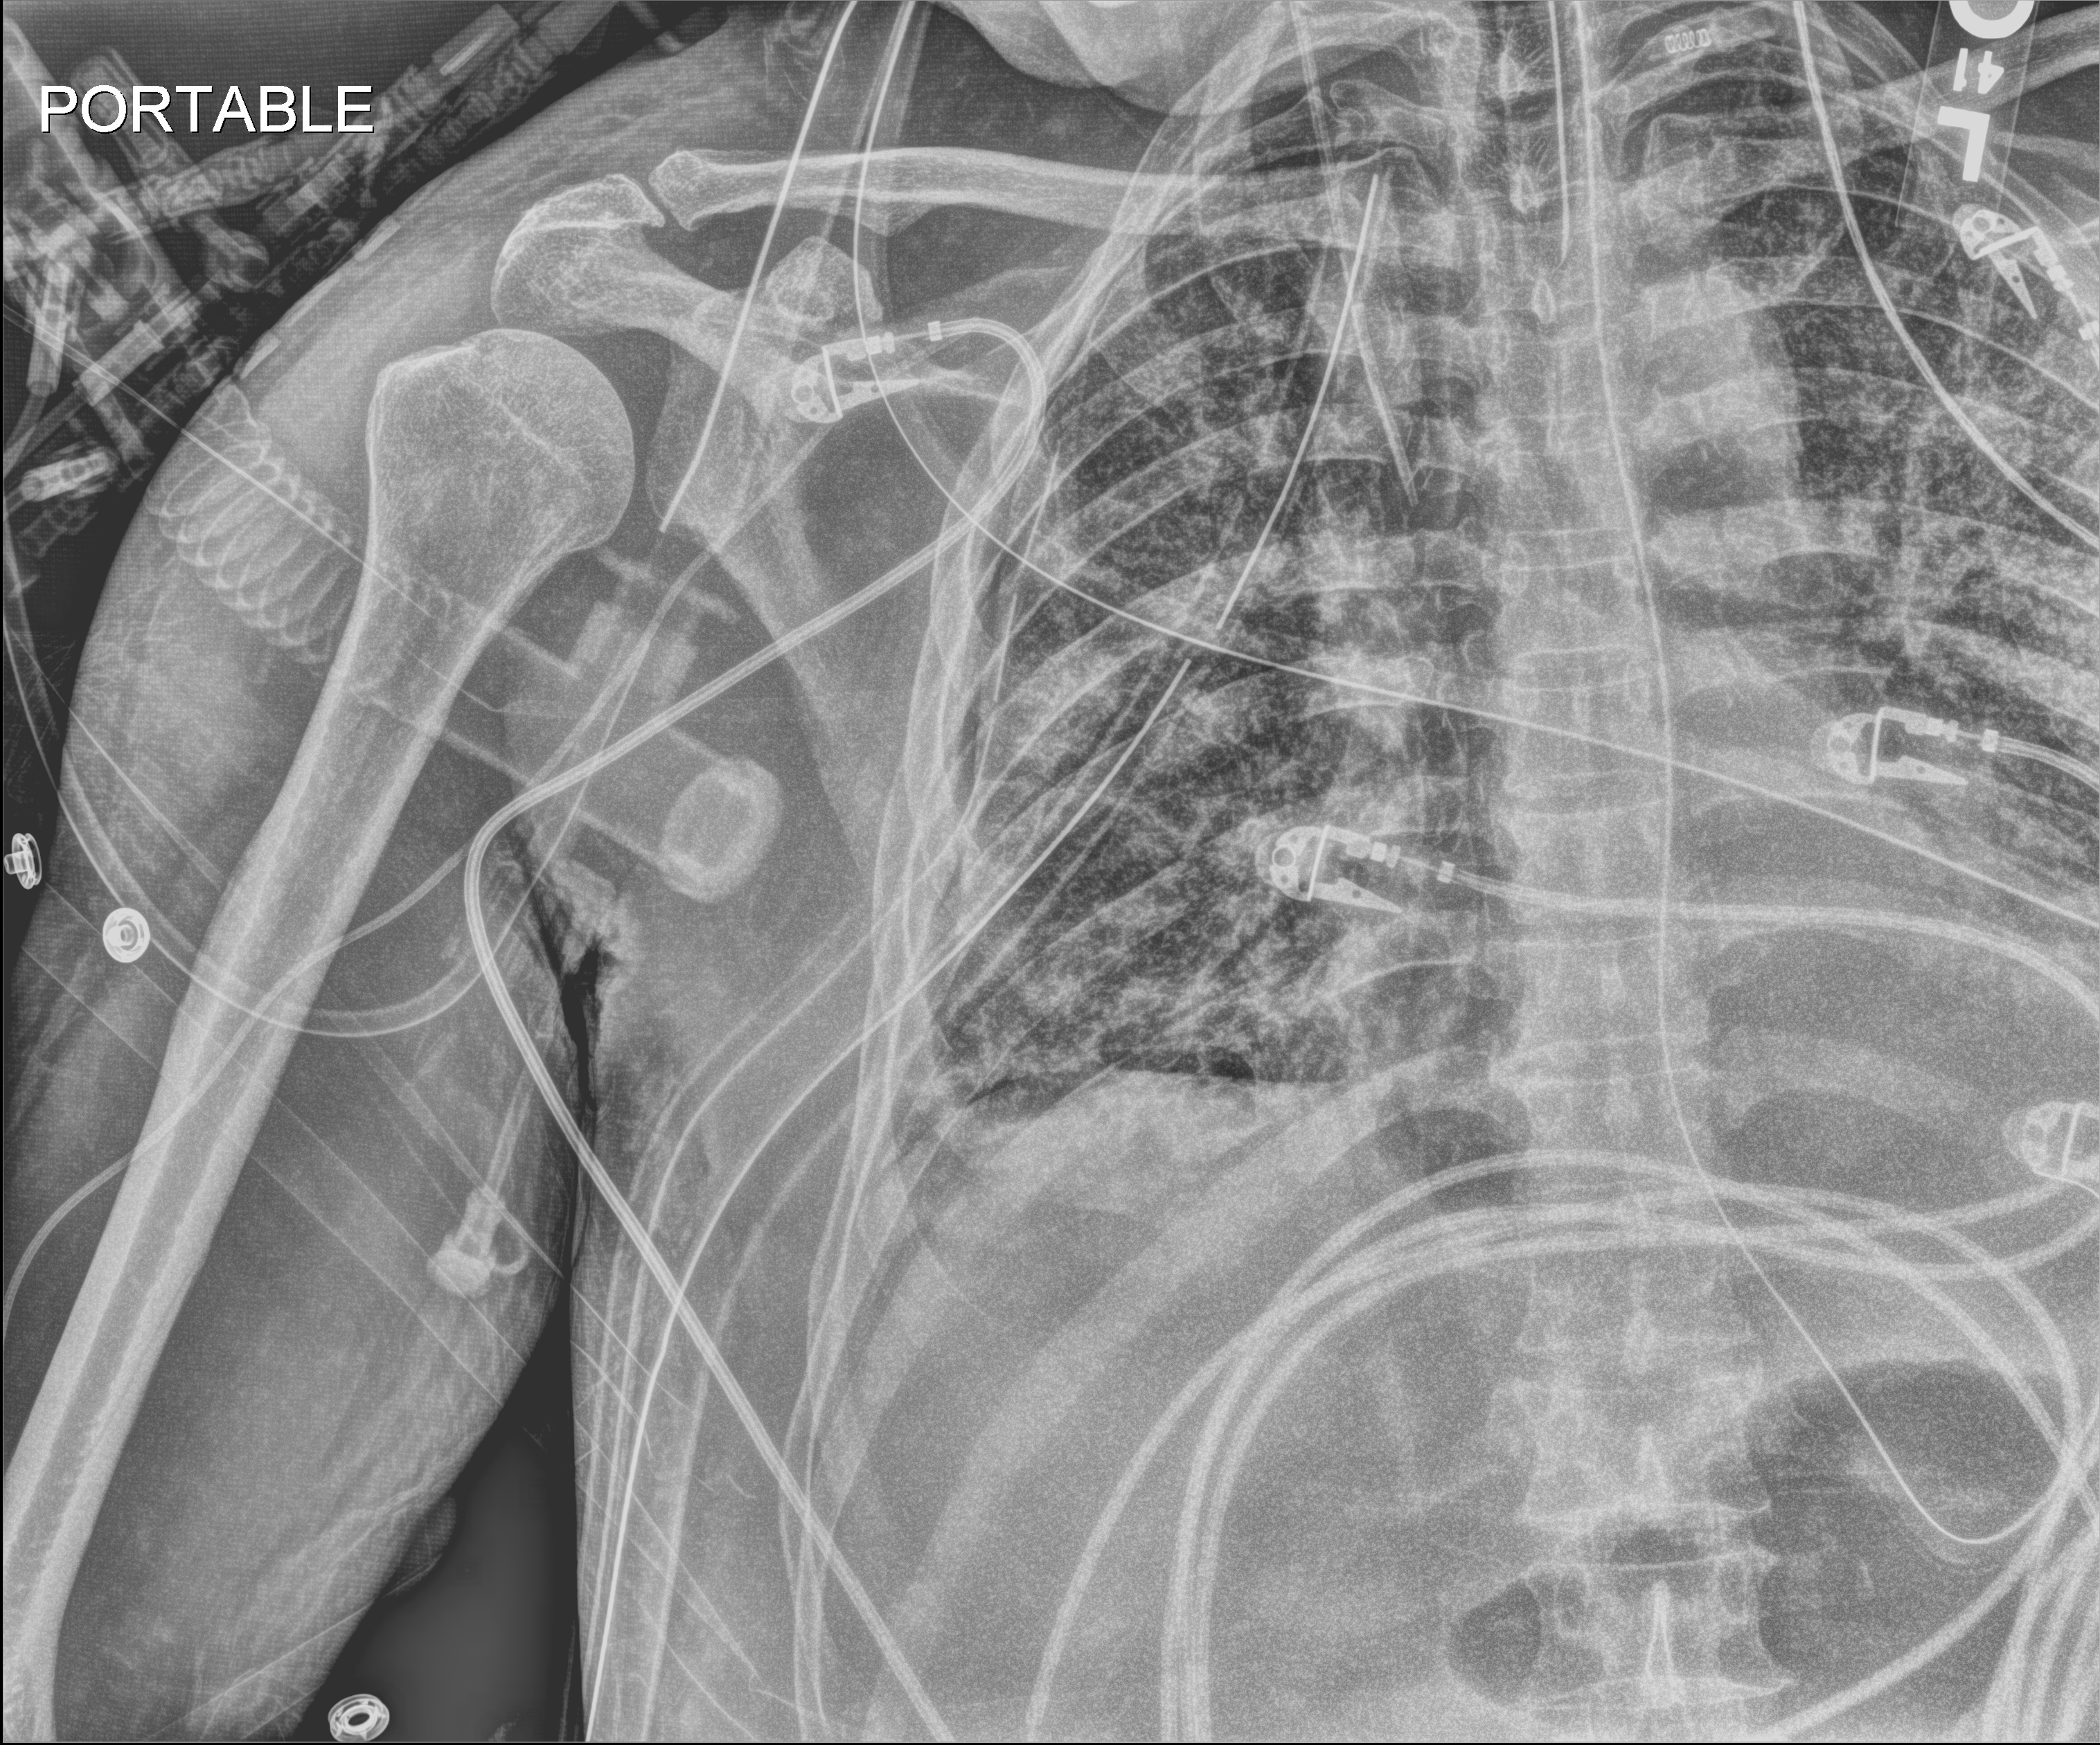
Portable chest radiograph, anteroposterior (AP) projection. Male patient hospitalised with COVID-19, age 60–74 years.
Hospital-stay facts (about this admission, not read from this image; timing relative to this image not recorded): other chronic lung disease (admission record): no.